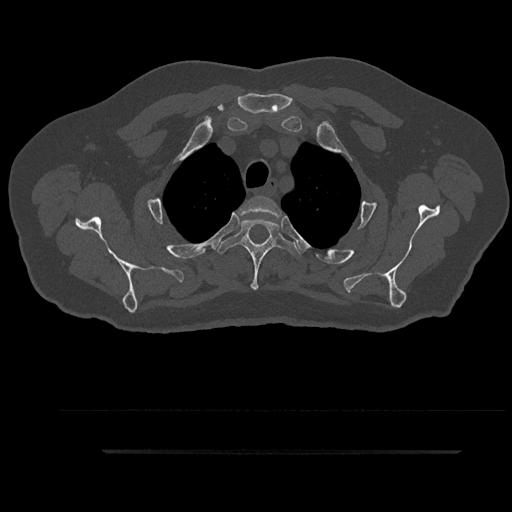
CT including the spine, one axial slice. Position 725 of 797 along the scan axis. Bone window (W 1800 / L 400 HU). 512 × 512 image matrix, field of view 432 × 432 mm. Patient: male, 63 years. Case-level facts recorded for this patient, not image findings: primary cancer: renal.
Outlined on this slice (semi-automatically segmented with operator editing):
- T2 vertebra: bounding box <238,196,282,218> (left, top, right, bottom; pixels)
- T3 vertebra: <216,218,301,290>